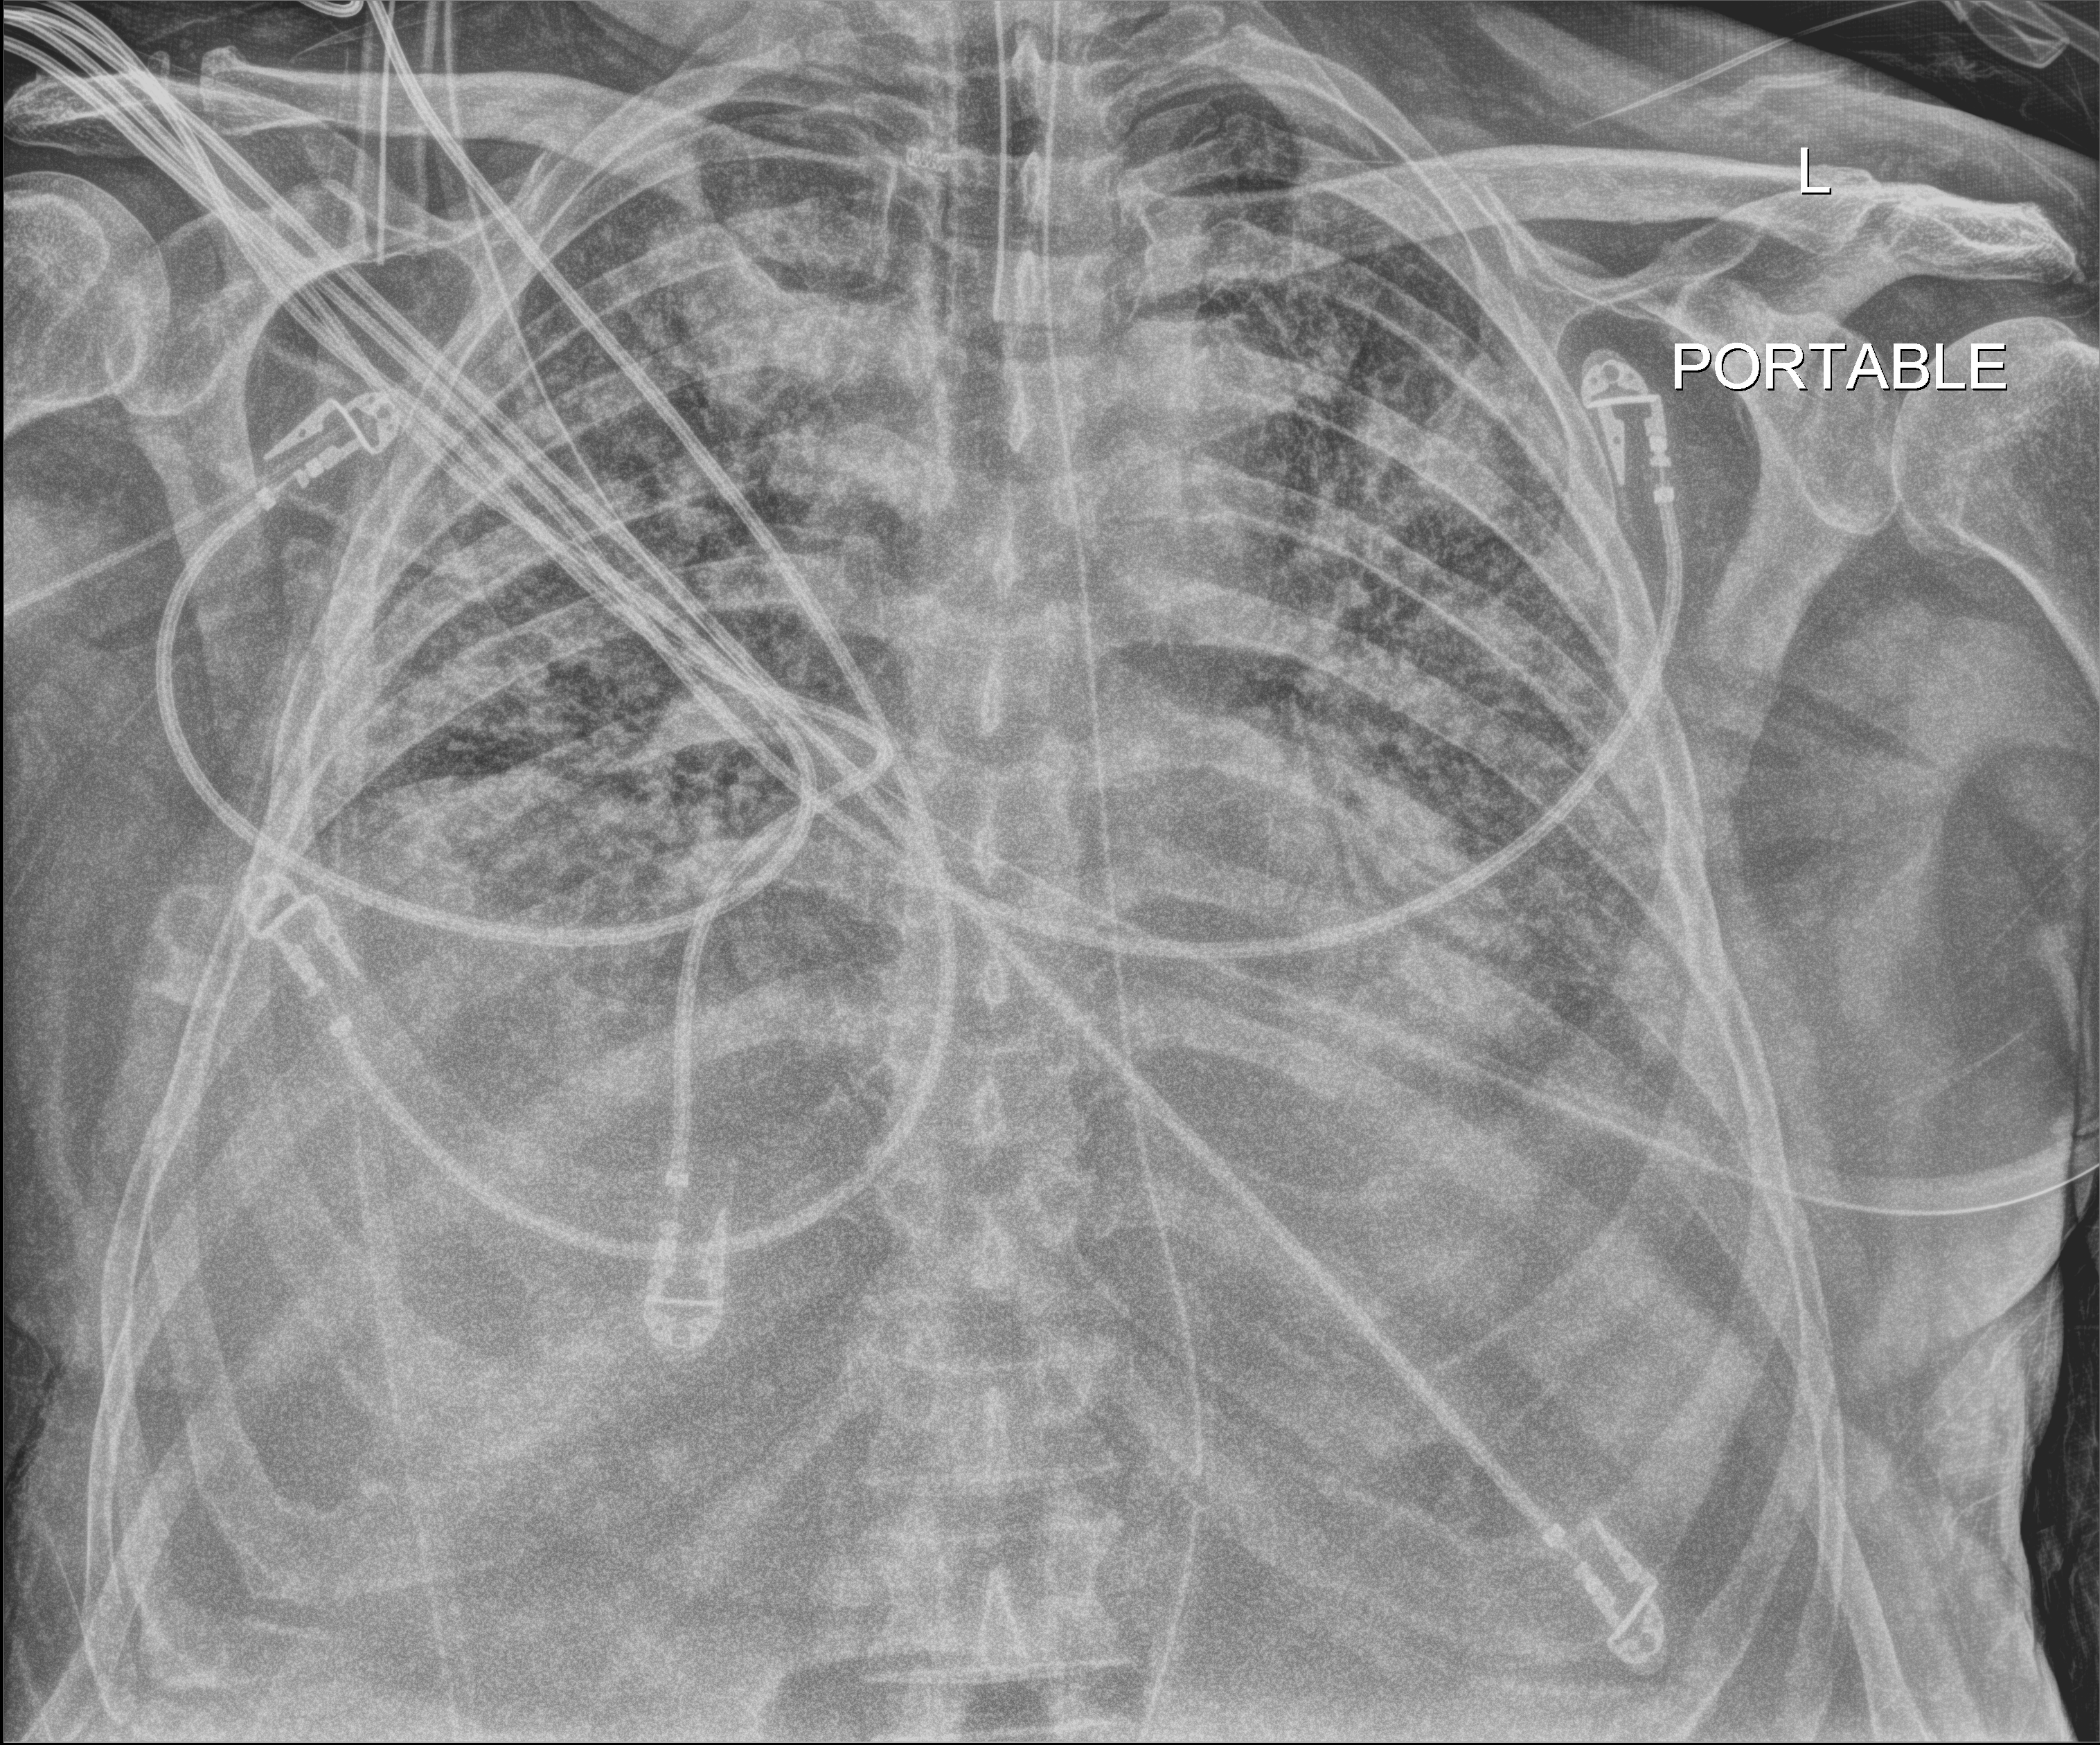
Portable chest radiograph; anteroposterior (AP) projection. Patient hospitalised with COVID-19; male, aged 60–74 years.
Admission-level facts for this patient (not findings on this image; timing relative to this image not recorded):
- admitted to intensive care during this hospital stay: yes